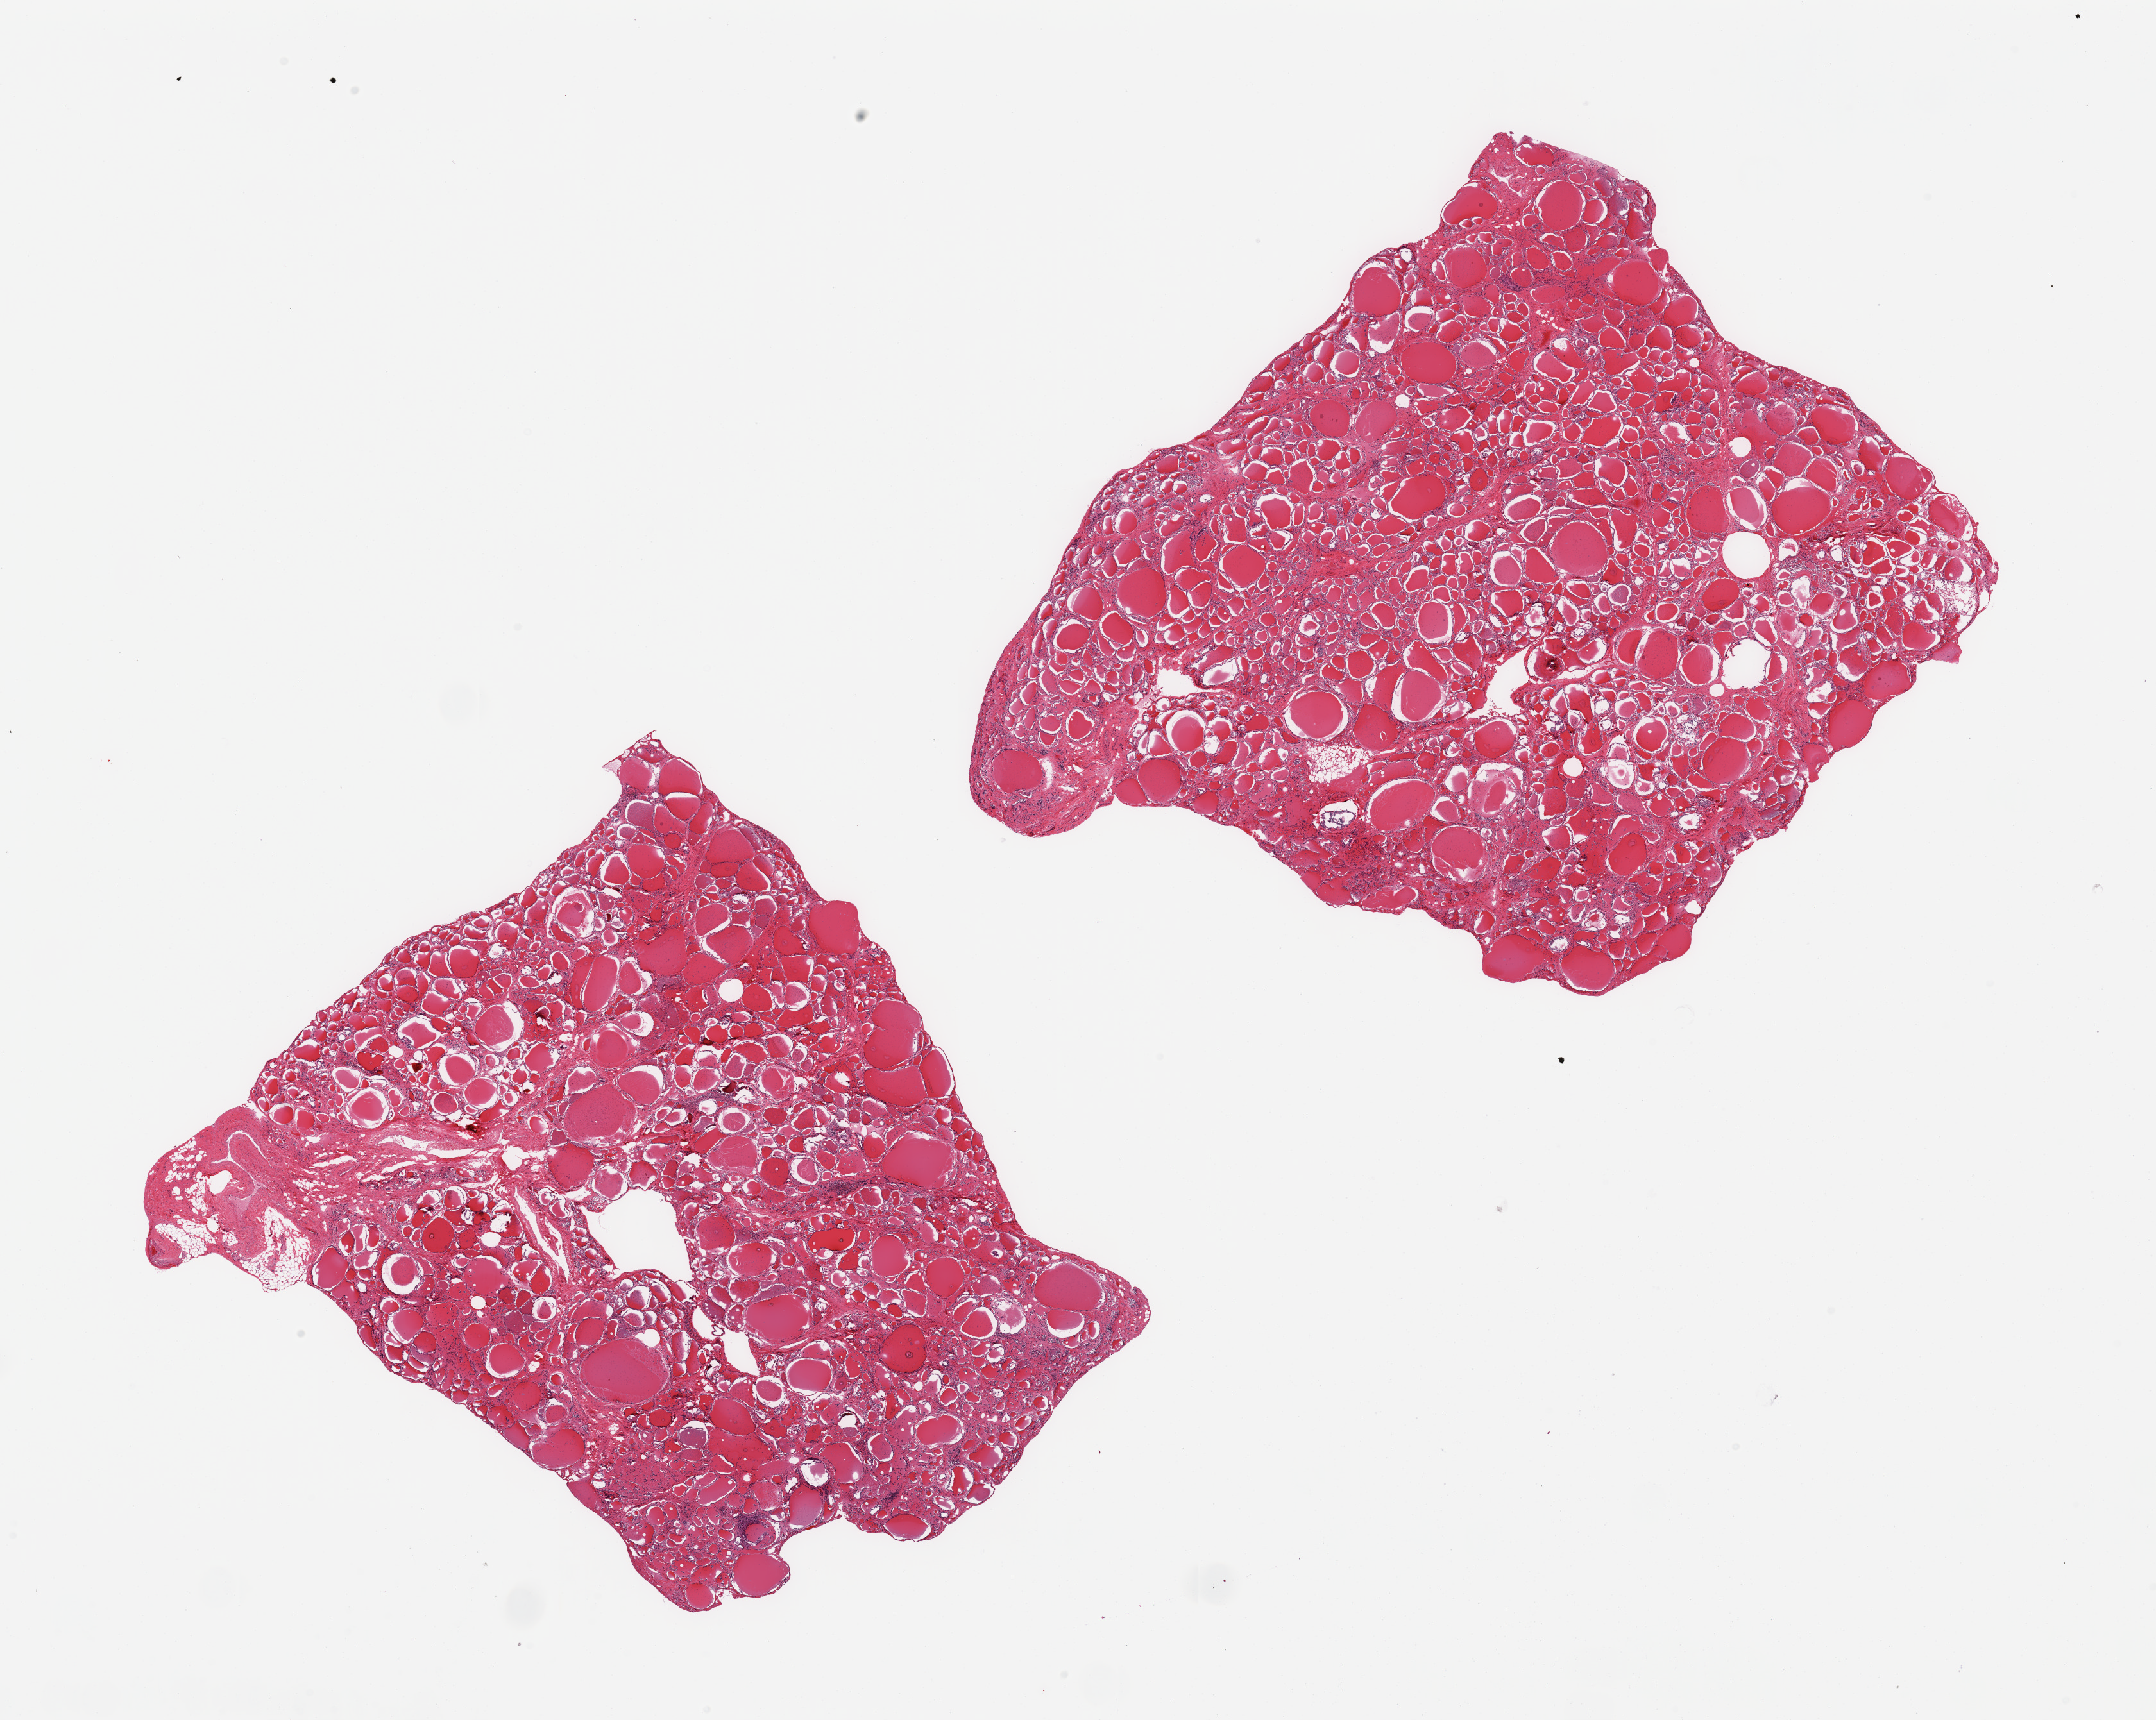
Whole-slide image, haematoxylin and eosin stain — a low-resolution overview of the entire scanned area, about 26.6 x 21.2 mm (slide scanned at 20x), PAXgene-fixed, paraffin-embedded tissue, sampled site (target tissue): thyroid, donor tissue sample. Donor sex: male.
Review note (as recorded): 2 pieces; well trimmed.